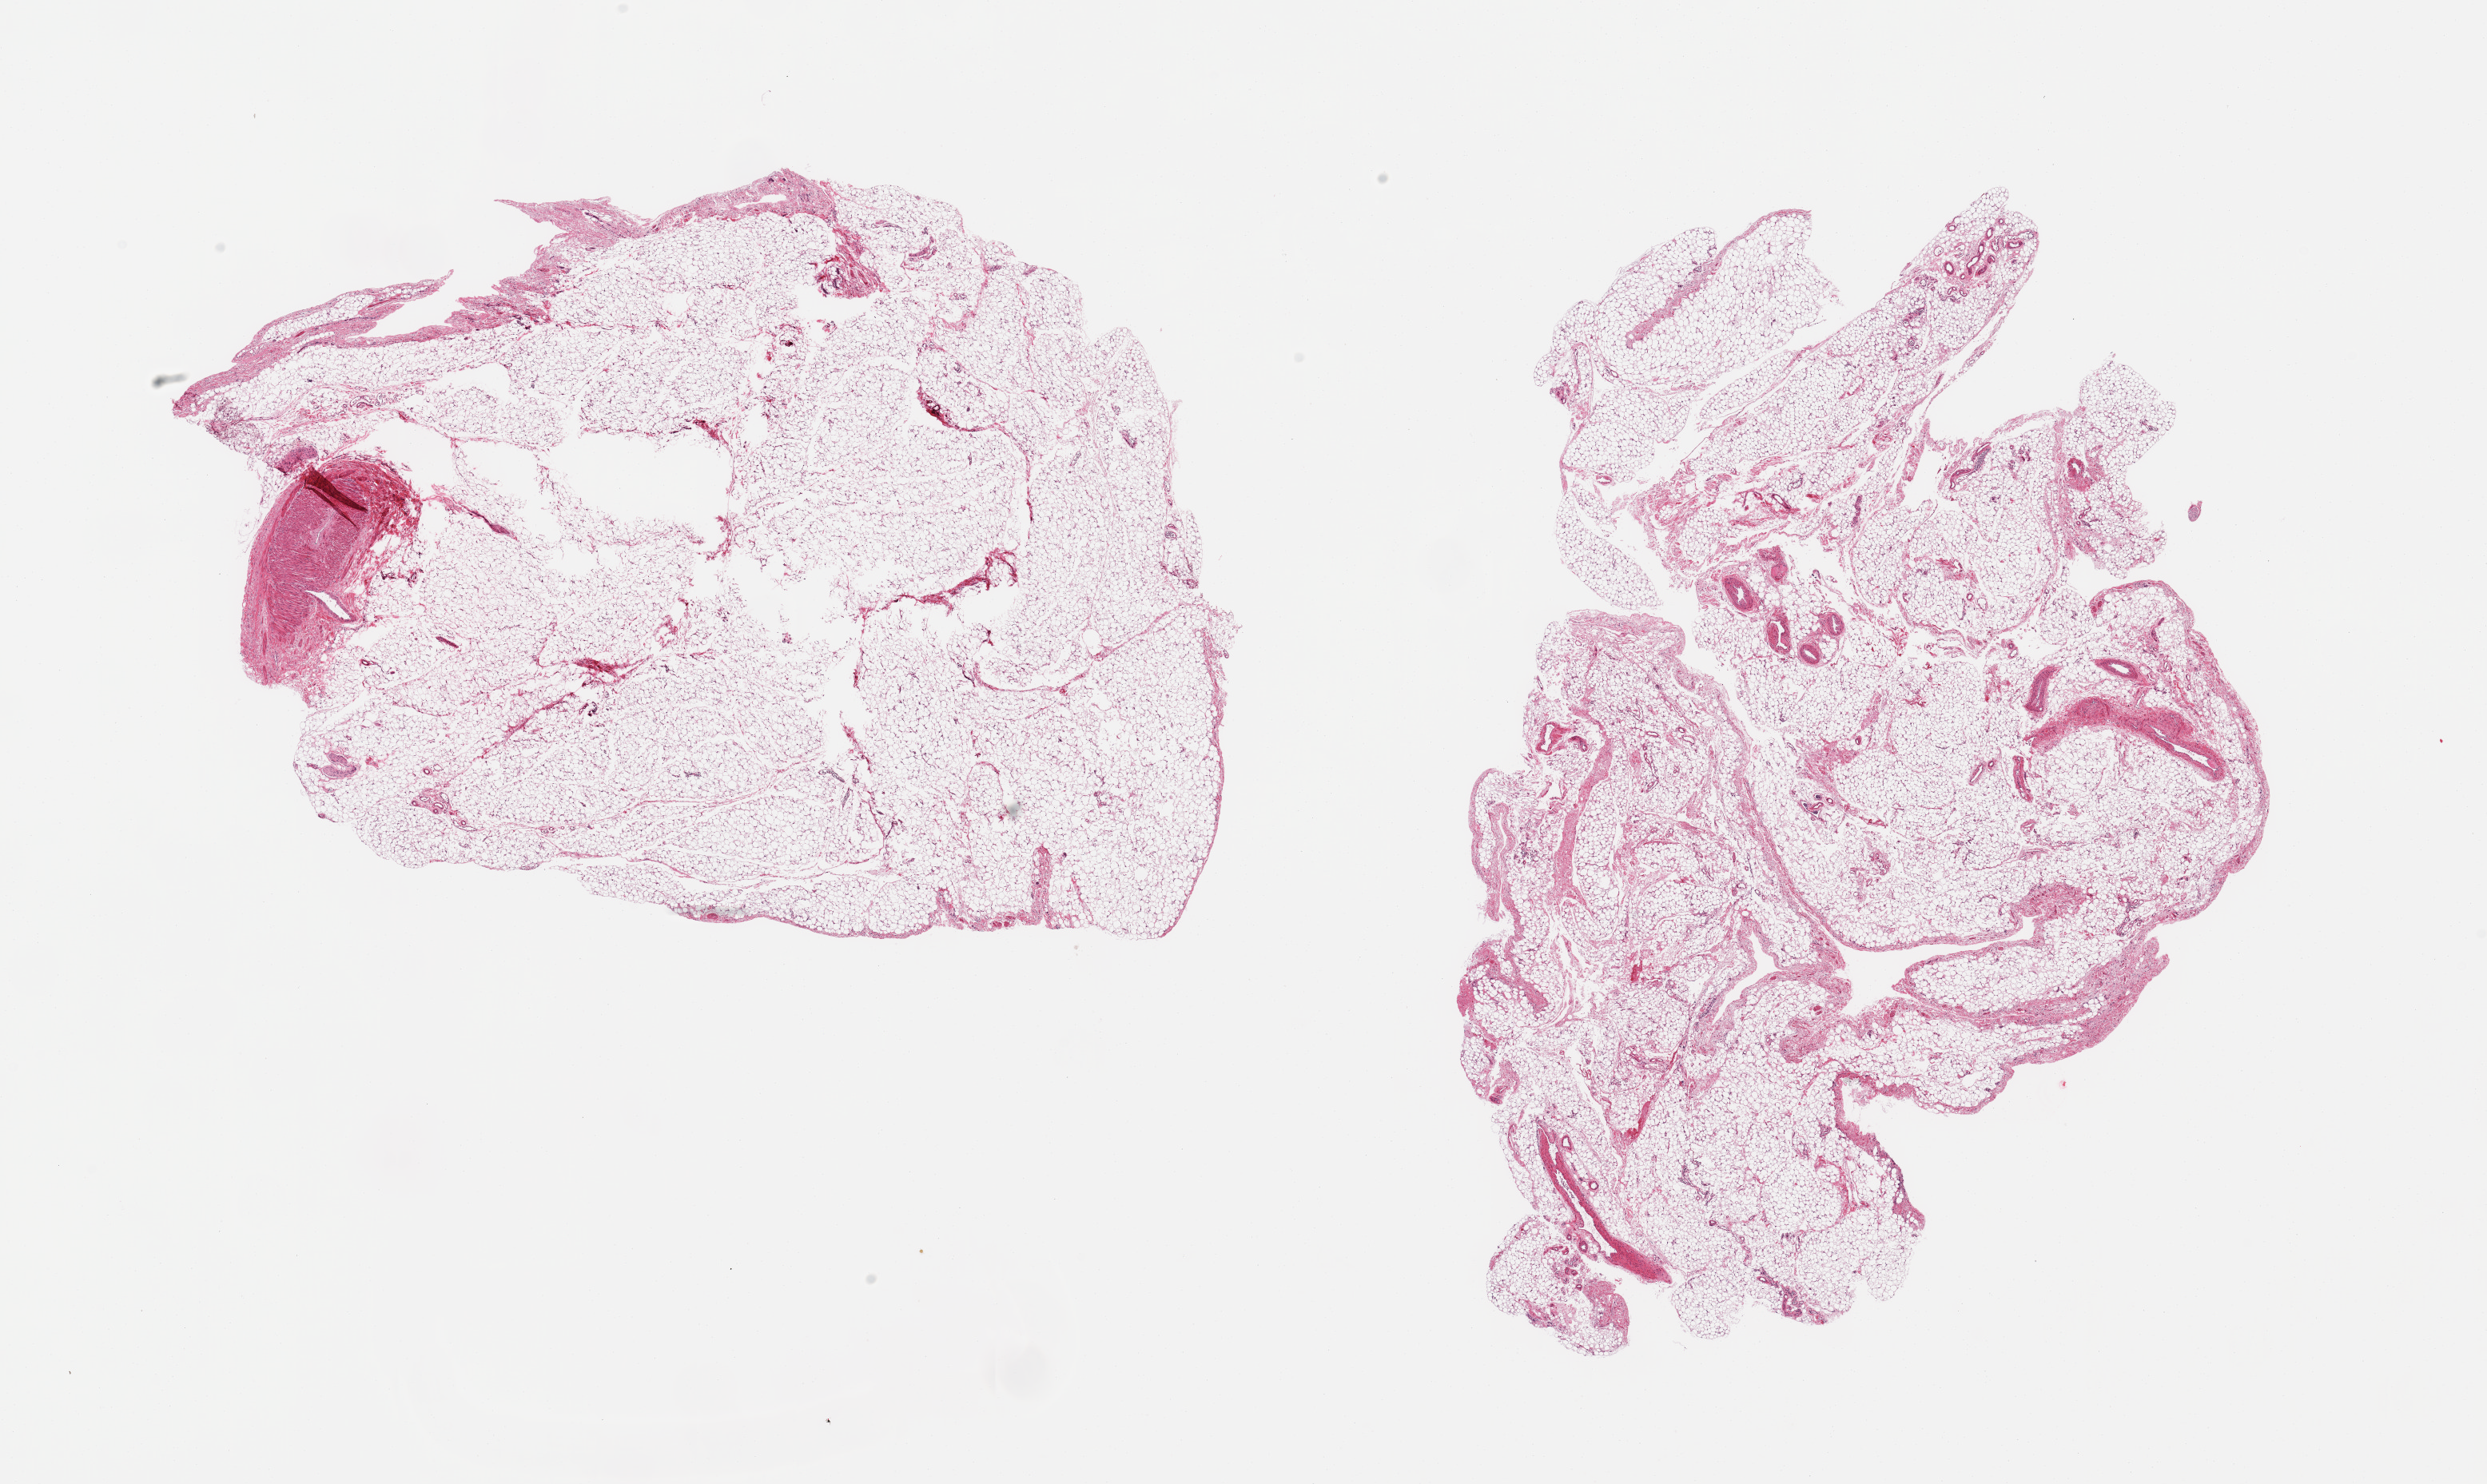
Digitized haematoxylin and eosin-stained section, brightfield, whole scanned area (about 24.6 x 14.7 mm) shown as a low-resolution overview. PAXgene-fixed paraffin-embedded (PFPE) section. Sampled site (target tissue): omentum. Donor tissue sample. Donor sex: female.
Reviewer comment on this tissue sample: 2 pieces; several prominent blood vessels.